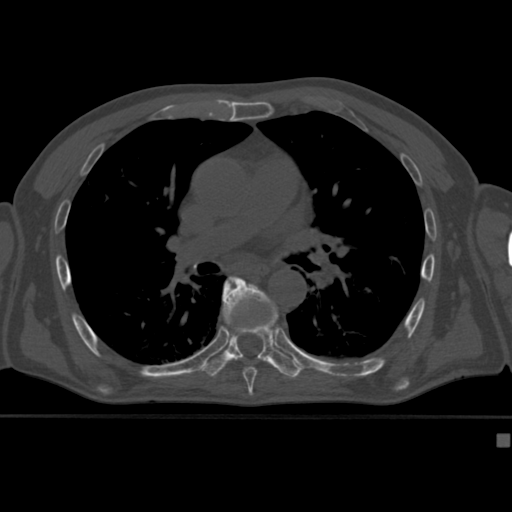
CT including the spine, one axial slice; slice 271 of 430 in the series (ordered by position); reconstruction kernel Br40s; 120 kVp; bone window (W 1800 / L 400 HU); 512 × 512 image matrix. Male patient, age 64 years. Case-level facts recorded for this patient, not image findings: primary cancer: uterus.
Annotated regions visible in this slice (semi-automatically segmented with operator editing):
- T7 vertebra: box from (x=223, y=275) to (x=270, y=382) px
- T8 vertebra: (x=205, y=276)–(x=302, y=381)